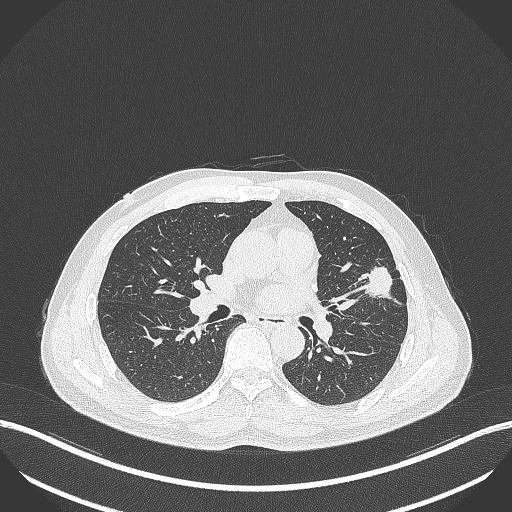
Chest CT, one axial slice. Reconstruction kernel B70f. Lung window (W 1500 / L -600 HU). 512 × 512 image matrix. Male patient, age 55 years. From the clinical record (not read from this slice): clinical TNM (as recorded): T1c N0 M0.
Annotated regions visible in this slice (bounding box drawn by a radiologist):
- lung tumour (recorded histology: adenocarcinoma): box from (x=360, y=261) to (x=406, y=305) px